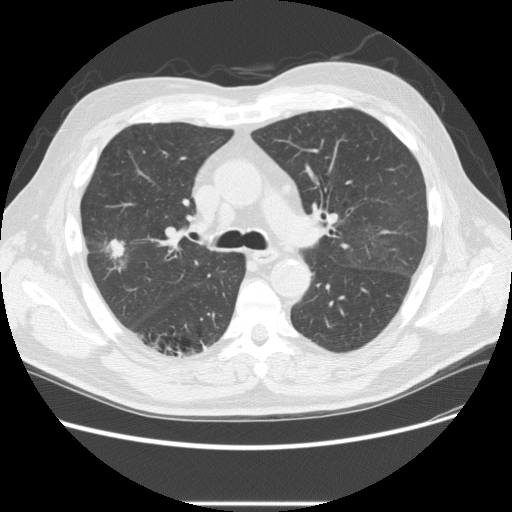
Low-dose screening chest CT, one axial slice. Reconstruction kernel STANDARD. Lung window (W 1500 / L -600 HU). 2.5 mm slice thickness. 512 × 512 image matrix.
Annotated regions visible in this slice (expert manual segmentation):
- lesion 2 (tumor, upper lobe of right lung): box from (x=106, y=239) to (x=125, y=260) px